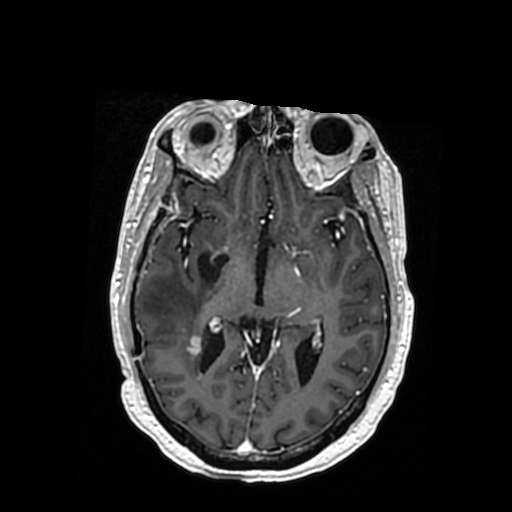
Brain MRI from a brain-tumour surgery series, one axial slice. T1-weighted post-contrast. 512 × 512 image matrix, field of view 260 × 260 mm. From the clinical record (not read from this slice): histopathology: Oligodendroglioma; WHO grade: 3; IDH mutation: yes; tumour location: Right Posterior Temporal Inferior Parietal.
Annotated regions visible in this slice (manually delineated by an expert):
- previous resection cavity: box from (x=197, y=252) to (x=228, y=281) px
- tumour: (x=183, y=333)–(x=198, y=351)